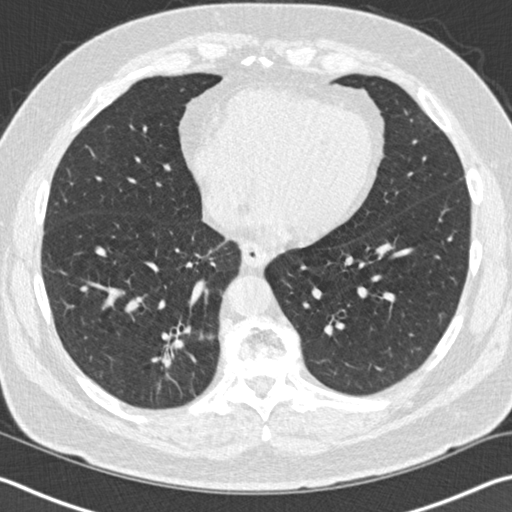
Low-dose screening chest CT, one axial slice; position 38 of 141 along the scan axis; reconstruction kernel B30f; 120 kVp; lung window (W 1500 / L -600 HU); 2 mm slice thickness; 512 × 512 image matrix, field of view 344 × 344 mm.
Annotated regions visible in this slice (outlined manually by an expert reader):
- lesion 1 (tumor, lower lobe of right lung): box from (x=152, y=337) to (x=187, y=368) px